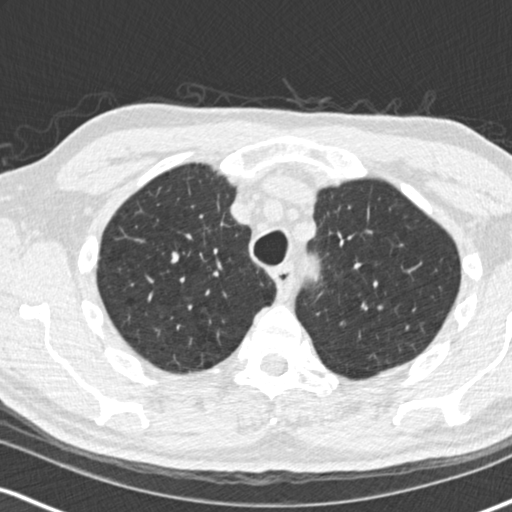
Low-dose screening chest CT, one axial slice; slice 122 of 170 in the series (ordered by position); reconstruction kernel B30f; lung window (W 1500 / L -600 HU); 2 mm slice thickness; 512 × 512 image matrix, field of view 320 × 320 mm.
Structures marked on this image (outlined manually by an expert reader):
- lesion 1 (tumor, upper lobe of right lung): bounding box <171,252,179,263> (left, top, right, bottom; pixels)